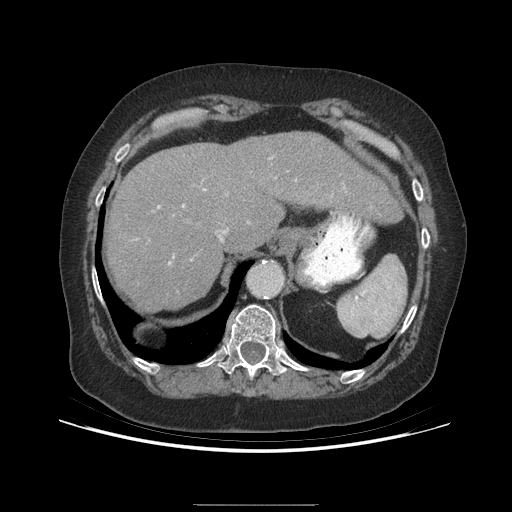
Contrast-enhanced abdominal CT (liver protocol), one axial slice. Slice 170 of 192 in the series (ordered by position). 140 kVp. Soft-tissue window (W 400 / L 40 HU). 2.5 mm slice thickness. 512 × 512 image matrix, field of view 400 × 400 mm. Case-level facts recorded for this patient, not image findings: diagnosis: hepatocellular carcinoma (patient treated with transarterial chemoembolisation; whether this scan precedes or follows treatment is not stated here); TNM stage (as recorded): Stage-I; Child-Pugh class: A; tumour differentiation: moderately differentiated.
Annotated regions visible in this slice (semi-automatic segmentation, software-assisted and operator-edited):
- liver parenchyma outside the tumour (the mass and vessels are separate outlines, so this box may not span the whole liver): bounding box <106,132,401,312> (left, top, right, bottom; pixels)
- liver vessels: <157,189,226,264>